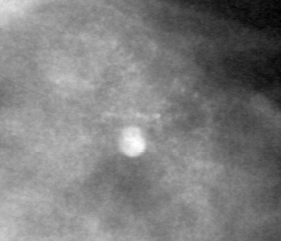
Region of interest cut from a scanned film mammogram (one marked finding), right breast, CC view.
Finding: calcifications, morphology pleomorphic, distribution clustered; BI-RADS assessment category 4; pathology (as recorded): benign.